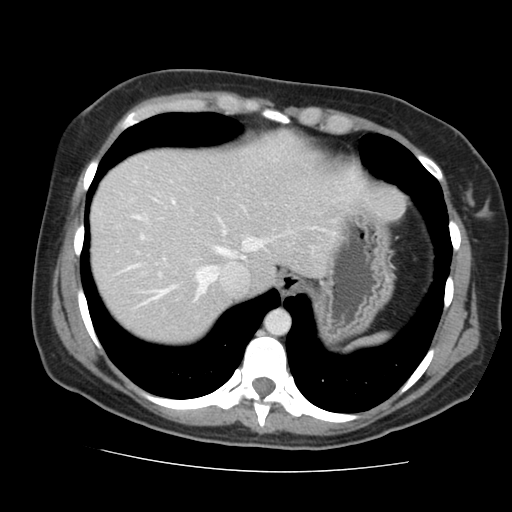
Contrast-enhanced abdominal CT, one axial slice; slice 126 of 144 in the series (ordered by position); 120 kVp; intravenous contrast given; soft-tissue window (W 400 / L 40 HU); 2.5 mm slice thickness; 512 × 512 image matrix, field of view 333 × 333 mm. Female patient, age 46 years. Case-level facts recorded for this patient, not image findings: diagnosis: colorectal cancer liver metastases, imaged before liver resection; multiple liver metastases: no; largest metastasis: 2.8 cm; disease in both lobes: no.
Structures marked on this image (expert manual segmentation):
- hepatic veins: bounding box <136,194,349,303> (left, top, right, bottom; pixels)
- liver: <91,134,343,343>
- planned liver remnant (the part of the liver to remain after resection): <91,134,343,343>